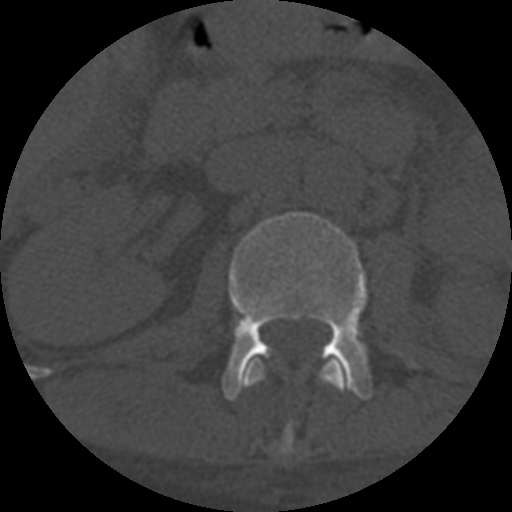
CT including the spine, one axial slice; slice 269 of 708 in the series (ordered by position); 120 kVp; one of 3 acquisitions stored at this slice position; bone window (W 1800 / L 400 HU); 512 × 512 image matrix. Patient age 55 years. Case-level facts recorded for this patient, not image findings: primary cancer: colon; vertebrae with lytic lesions (as recorded): T12, L1, L5.
Annotated regions visible in this slice (semi-automatic segmentation, software-assisted and operator-edited):
- L1 vertebra: bounding box <243,357,347,456> (left, top, right, bottom; pixels)
- L2 vertebra: <222,212,420,400>